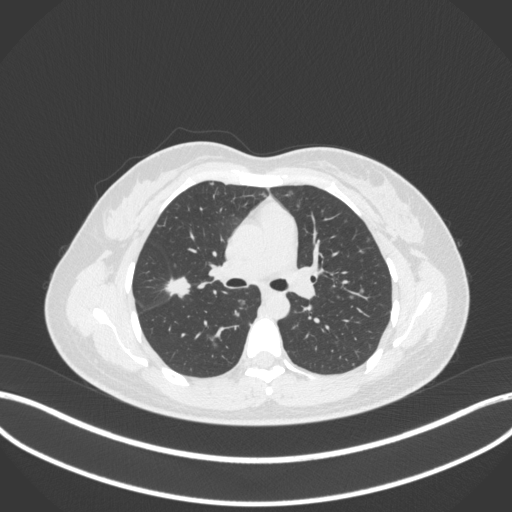
Chest CT, one axial slice; slice 205 of 214 in the series (ordered by position); 120 kVp; lung window (W 1500 / L -600 HU); 1 mm slice thickness; 512 × 512 image matrix. Patient: female, 33 years. Case-level facts recorded for this patient, not image findings: clinical TNM (as recorded): T1c N0 M0.
Outlined on this slice (bounding box drawn by a radiologist):
- lung tumour (recorded histology: adenocarcinoma): box from (x=161, y=273) to (x=193, y=306) px